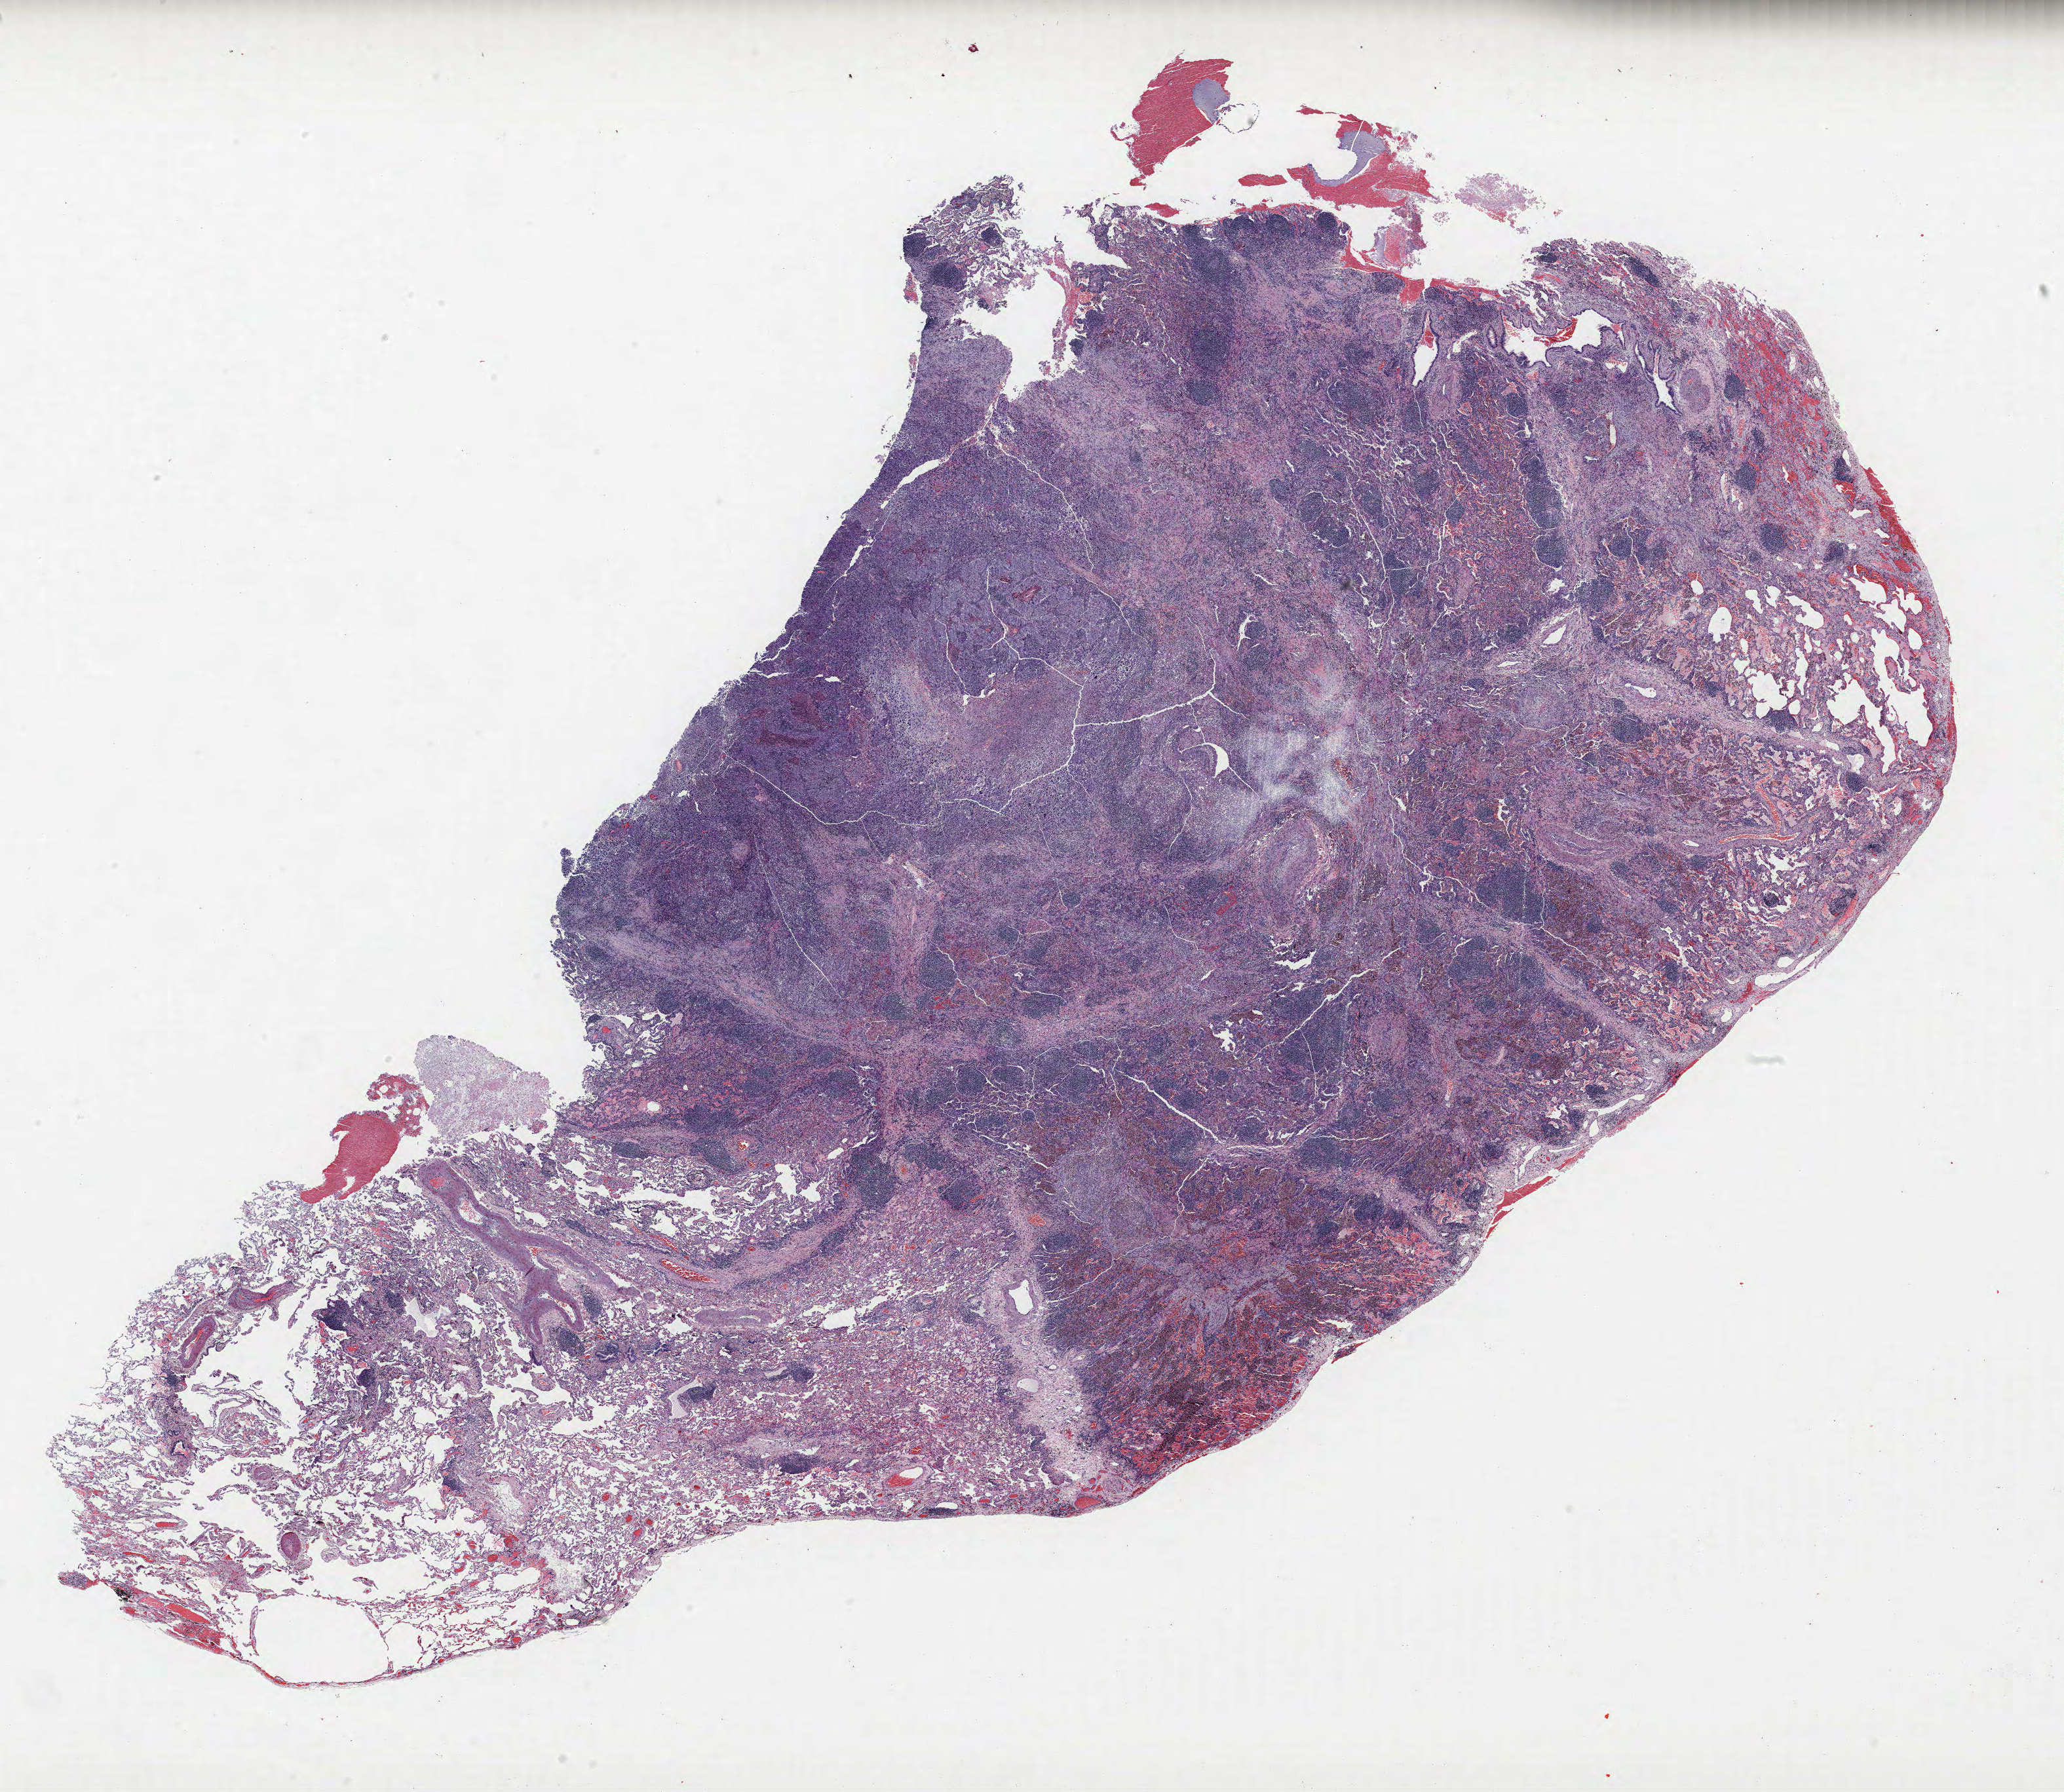
Hematoxylin and eosin (H&E) stained whole-slide image — whole scanned area (about 25.2 x 21.9 mm, slide scanned at 40x) shown as a low-resolution overview; FFPE section; lung. Male, age 63 at enrolment. Former smoker at enrolment. Grade: undifferentiated (G4).
Stage (AJCC 6th edition): IB. Primary tumour location (clinical record): right upper lobe. Participant's lung-cancer diagnosis: Large cell carcinoma, NOS (ICD-O-3 8012/3). ICD-O-3 topography: upper lobe of lung (C34.1). Tumour size (pathology): 45 mm.